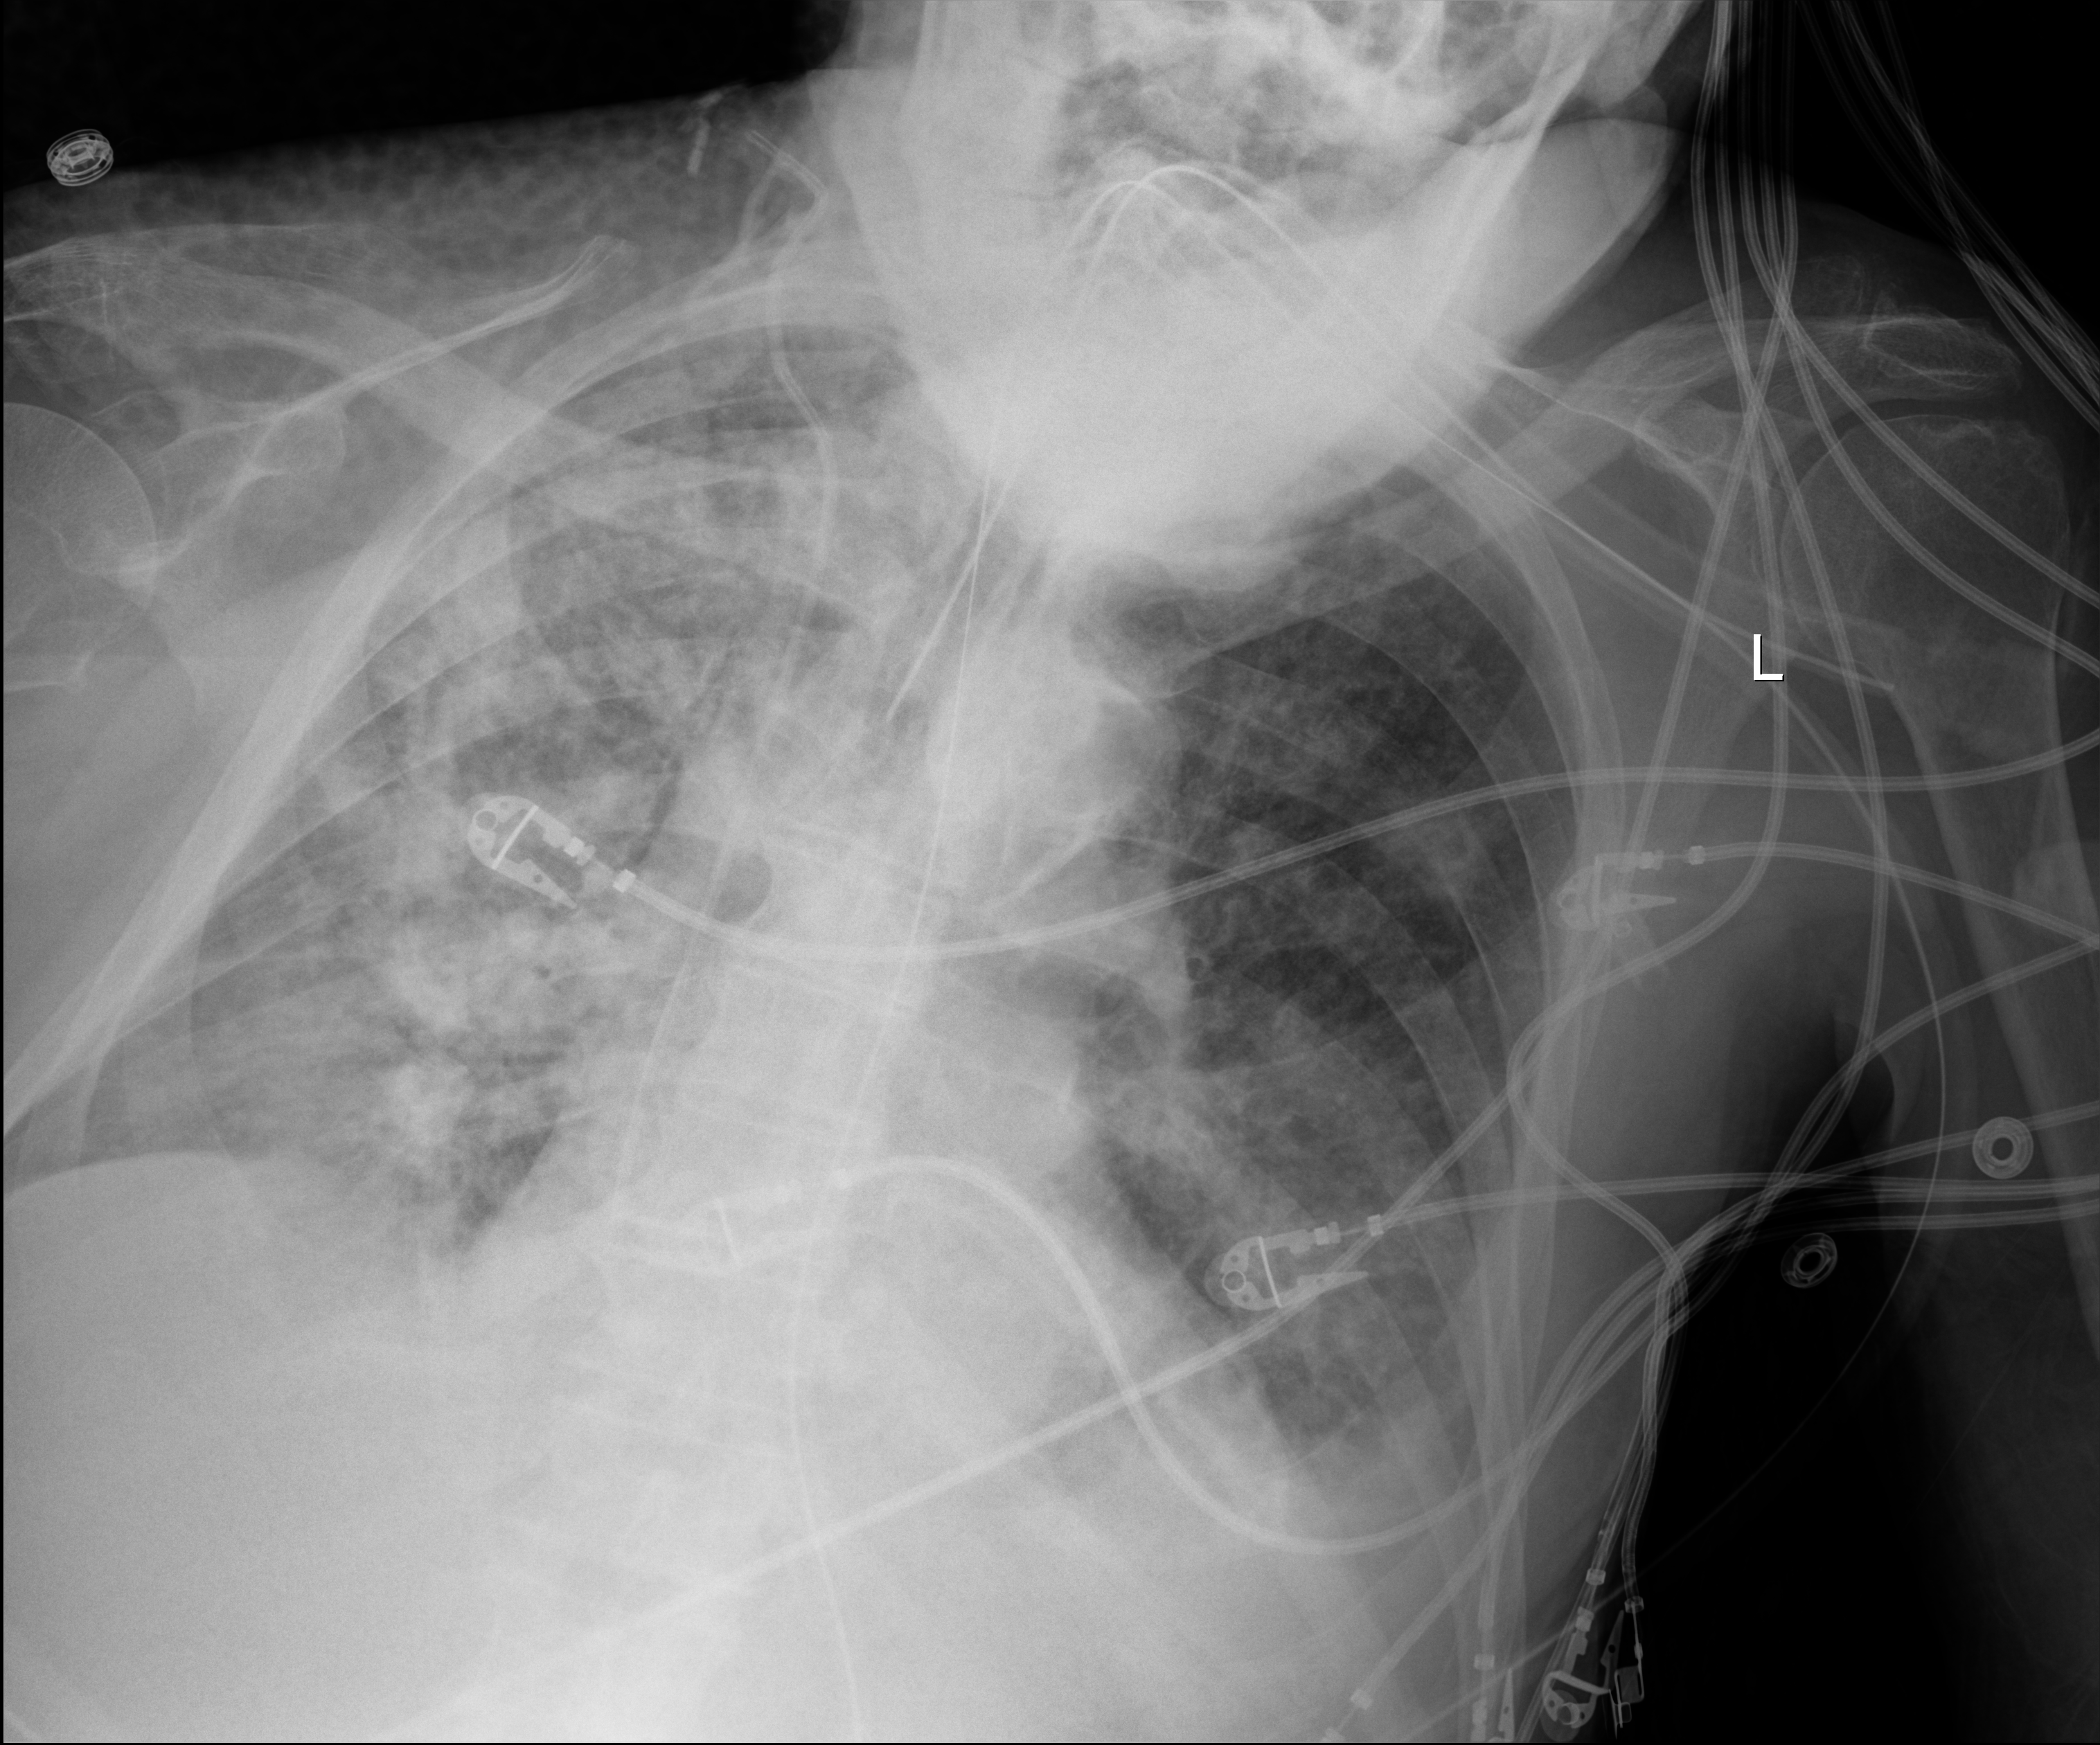
Portable chest radiograph, anteroposterior (AP) projection. Male patient hospitalised with COVID-19, age 75–90 years.
From the hospital-stay record, not from the radiograph (when in the stay this image was taken is not recorded): length of hospital stay: 28 days.